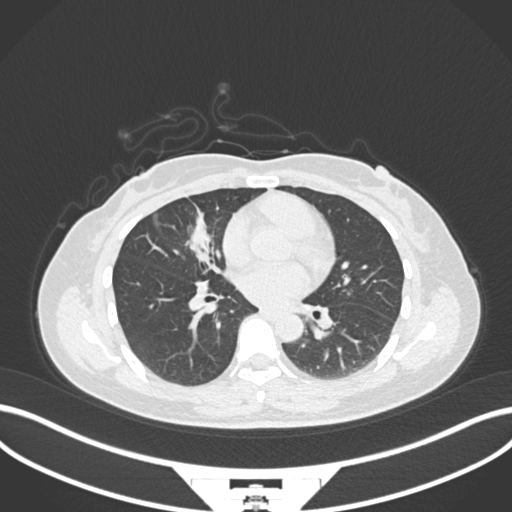
Chest CT, one axial slice. Slice 80 of 171 in the series (ordered by position). Reconstruction kernel B30f. 120 kVp. Lung window (W 1500 / L -600 HU). 1 mm slice thickness. 512 × 512 image matrix, field of view 400 × 400 mm. Patient: female, 43 years. Case-level facts recorded for this patient, not image findings: clinical TNM (as recorded): T1c N3 M1; histopathological grade: G1.
Outlined on this slice (rectangle marked by the reading radiologist):
- lung tumour (recorded histology: adenocarcinoma): box from (x=178, y=212) to (x=215, y=271) px